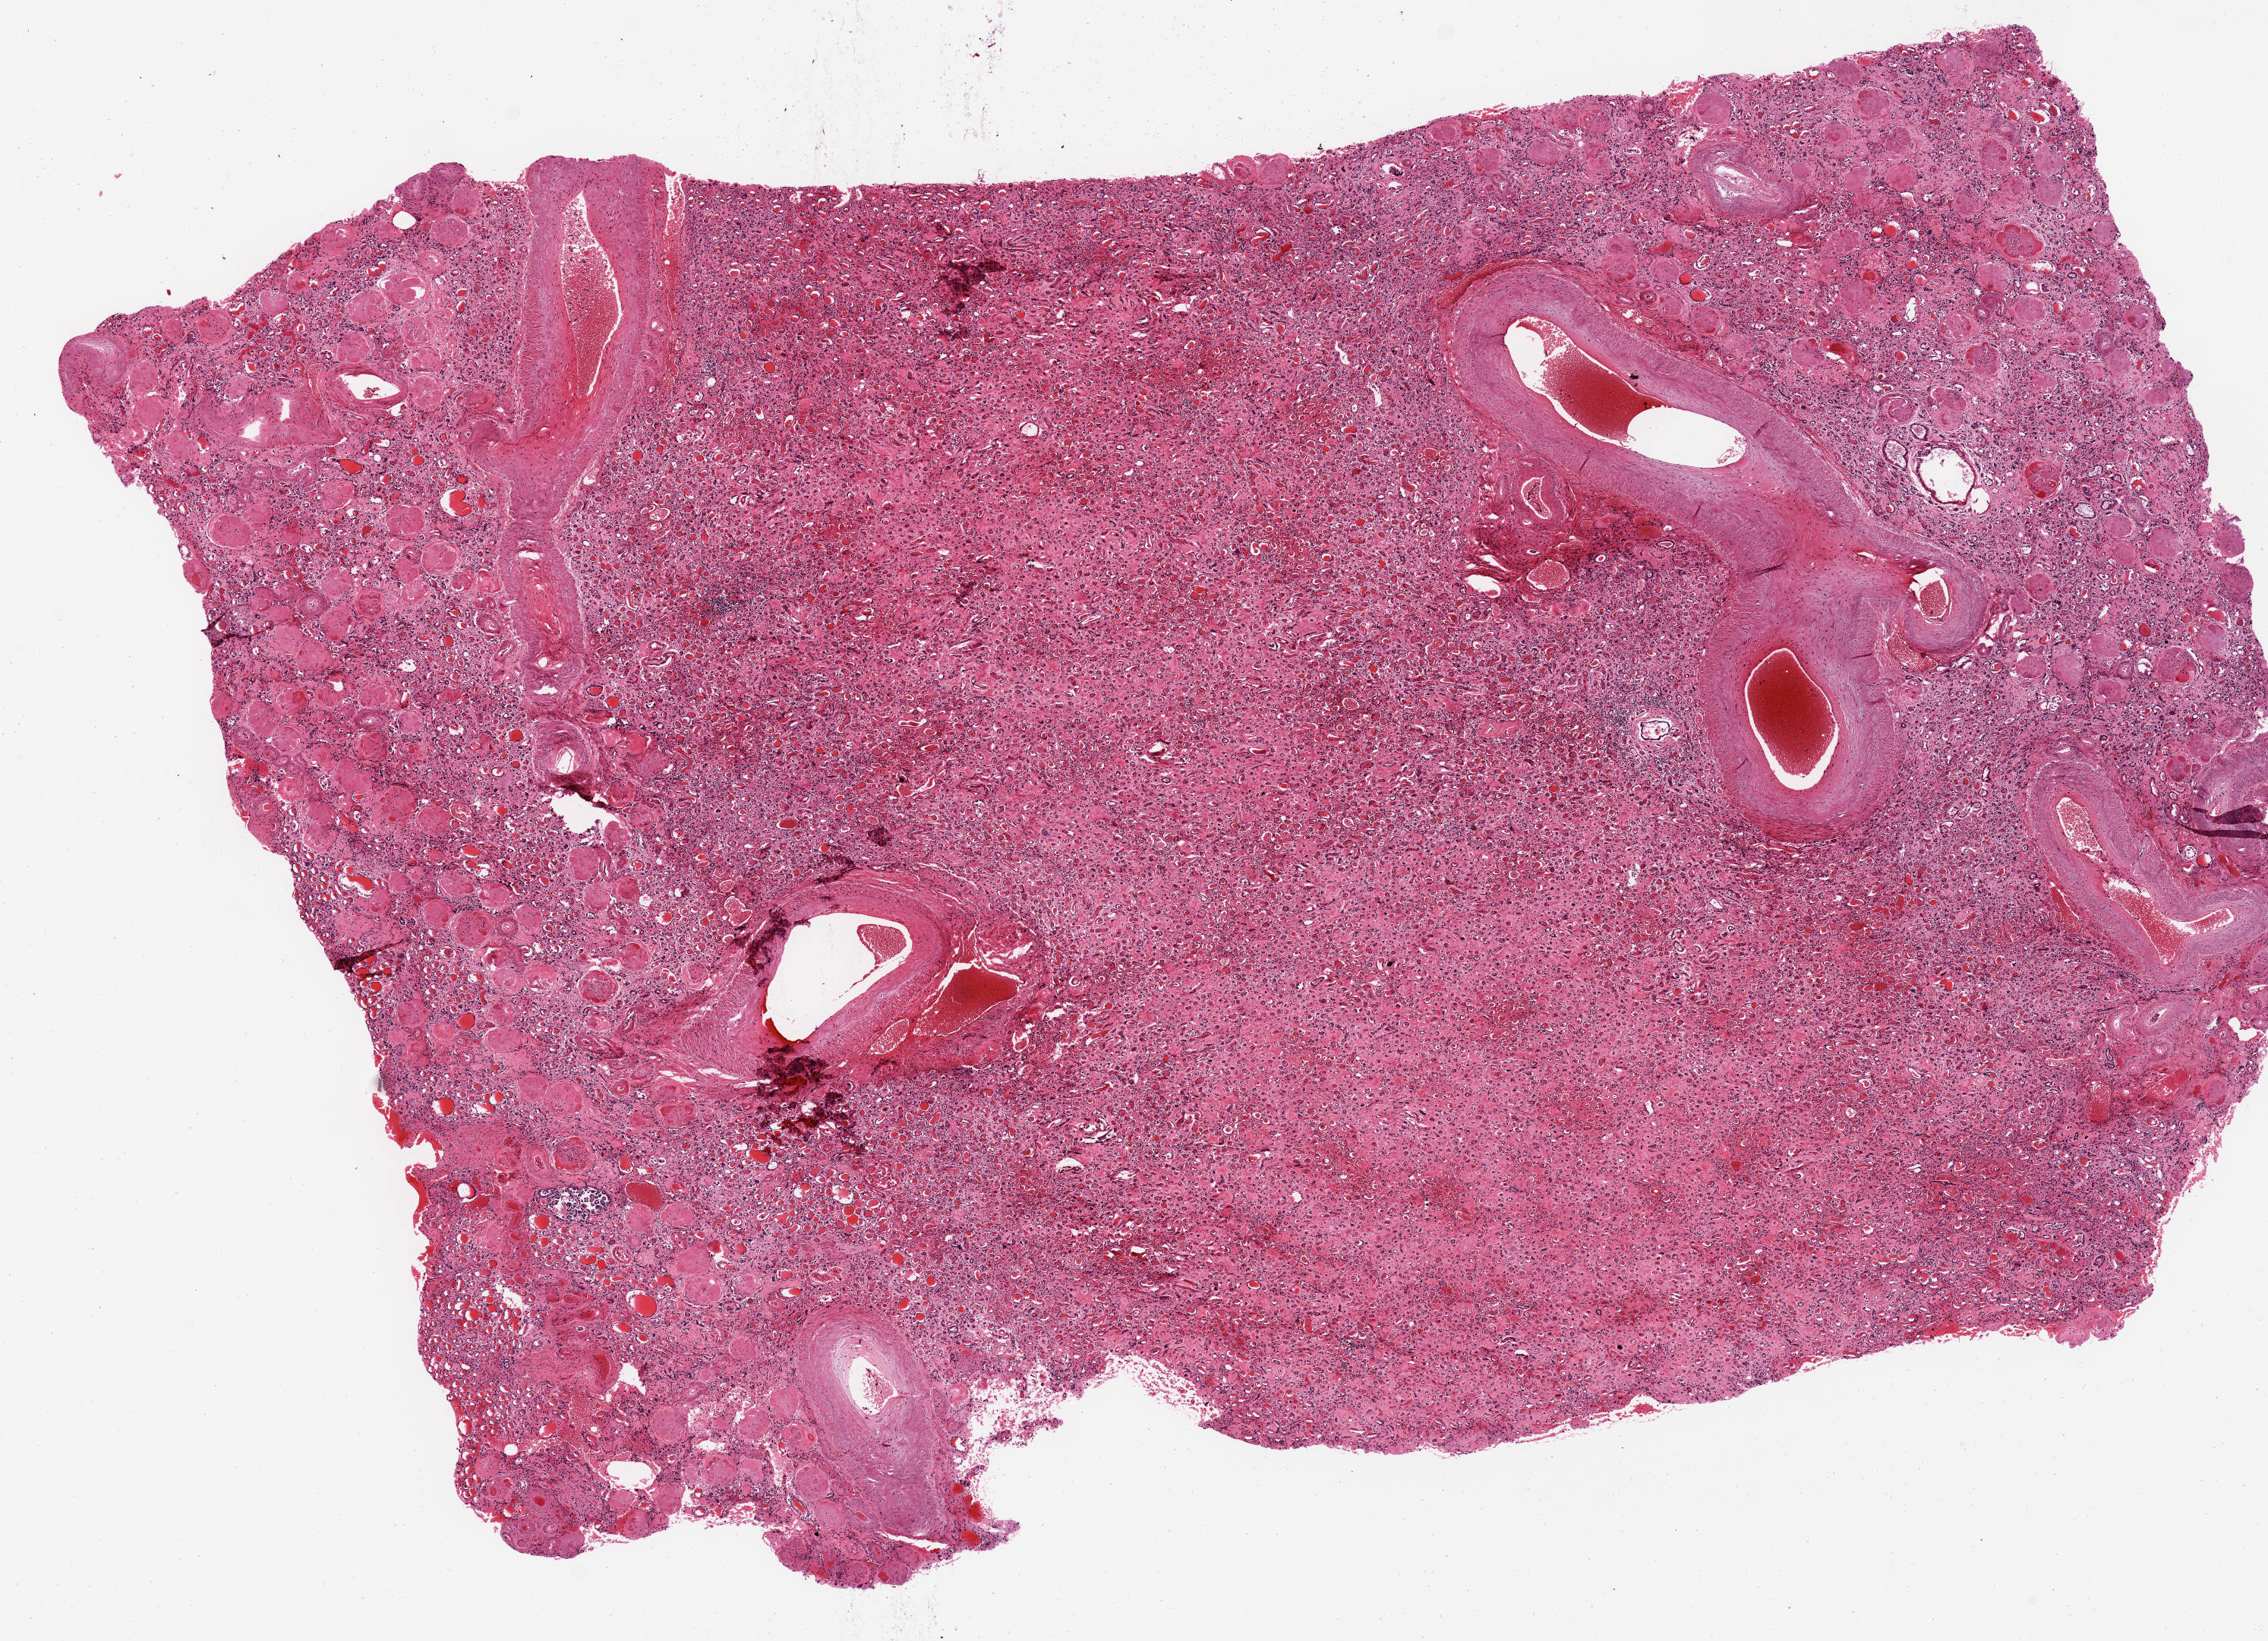
Whole-slide image, H&E stain, brightfield — low-resolution overview of the scanned area, about 11.8 x 8.5 mm (acquisition: 20x scan), PAXgene-fixed, paraffin-embedded tissue, target tissue: renal medulla, tissue donor sample. Female donor.
- review note (as recorded): Severe interstitial fibrosis; mild tubular autolysis (???score 1???); microadenoma <1mm